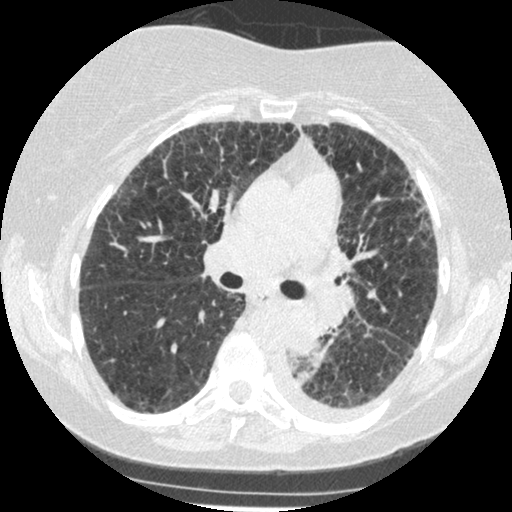
Low-dose screening chest CT, one axial slice. Slice 156 of 341 in the series (ordered by position). Lung window (W 1500 / L -600 HU). 1.25 mm slice thickness. 512 × 512 image matrix, field of view 310 × 310 mm.
Outlined on this slice (manually delineated by an expert):
- lesion 1 (tumor, lower lobe of left lung): bounding box (x1, y1, x2, y2) in pixels: (289, 307, 328, 357)